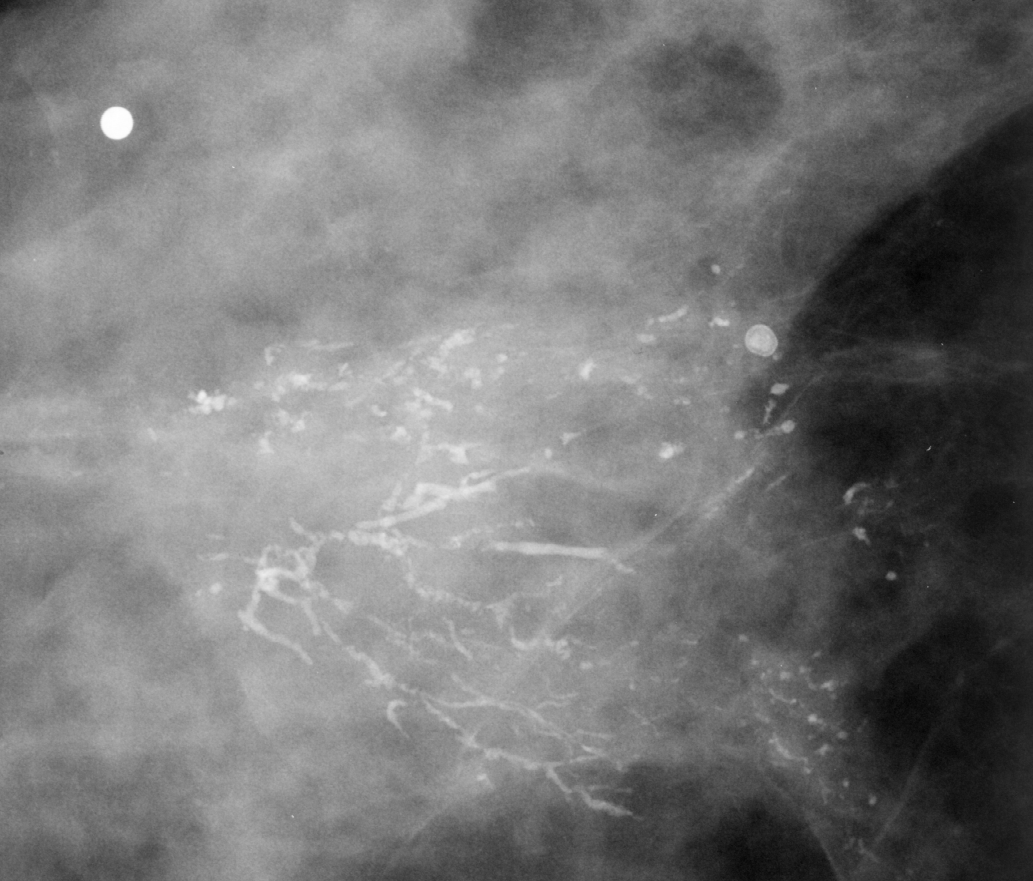
Crop from a digitized film mammogram around one marked abnormality; right breast; CC view; BI-RADS breast density category 3 (scale 1–4).
Finding: calcifications, morphology fine linear branching, distribution segmental; BI-RADS assessment category 5; pathology result (as recorded, not read from the image): malignant.